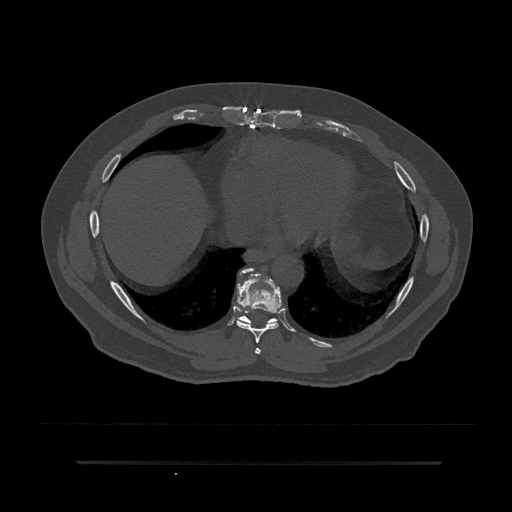
CT including the spine, one axial slice; reconstruction kernel Br40s/3; bone window (W 1800 / L 400 HU); 0.5 mm slice thickness; 512 × 512 image matrix, field of view 464 × 464 mm. Patient: male, 59 years. Case-level facts recorded for this patient, not image findings: primary cancer: bile ducts; vertebrae with lytic lesions (as recorded): T10.
Outlined on this slice (semi-automatic segmentation, software-assisted and operator-edited):
- T7 vertebra: bounding box [x1, y1, x2, y2] px = [255, 348, 261, 354]
- T8 vertebra: [236, 268, 282, 343]
- T9 vertebra: [237, 272, 279, 325]